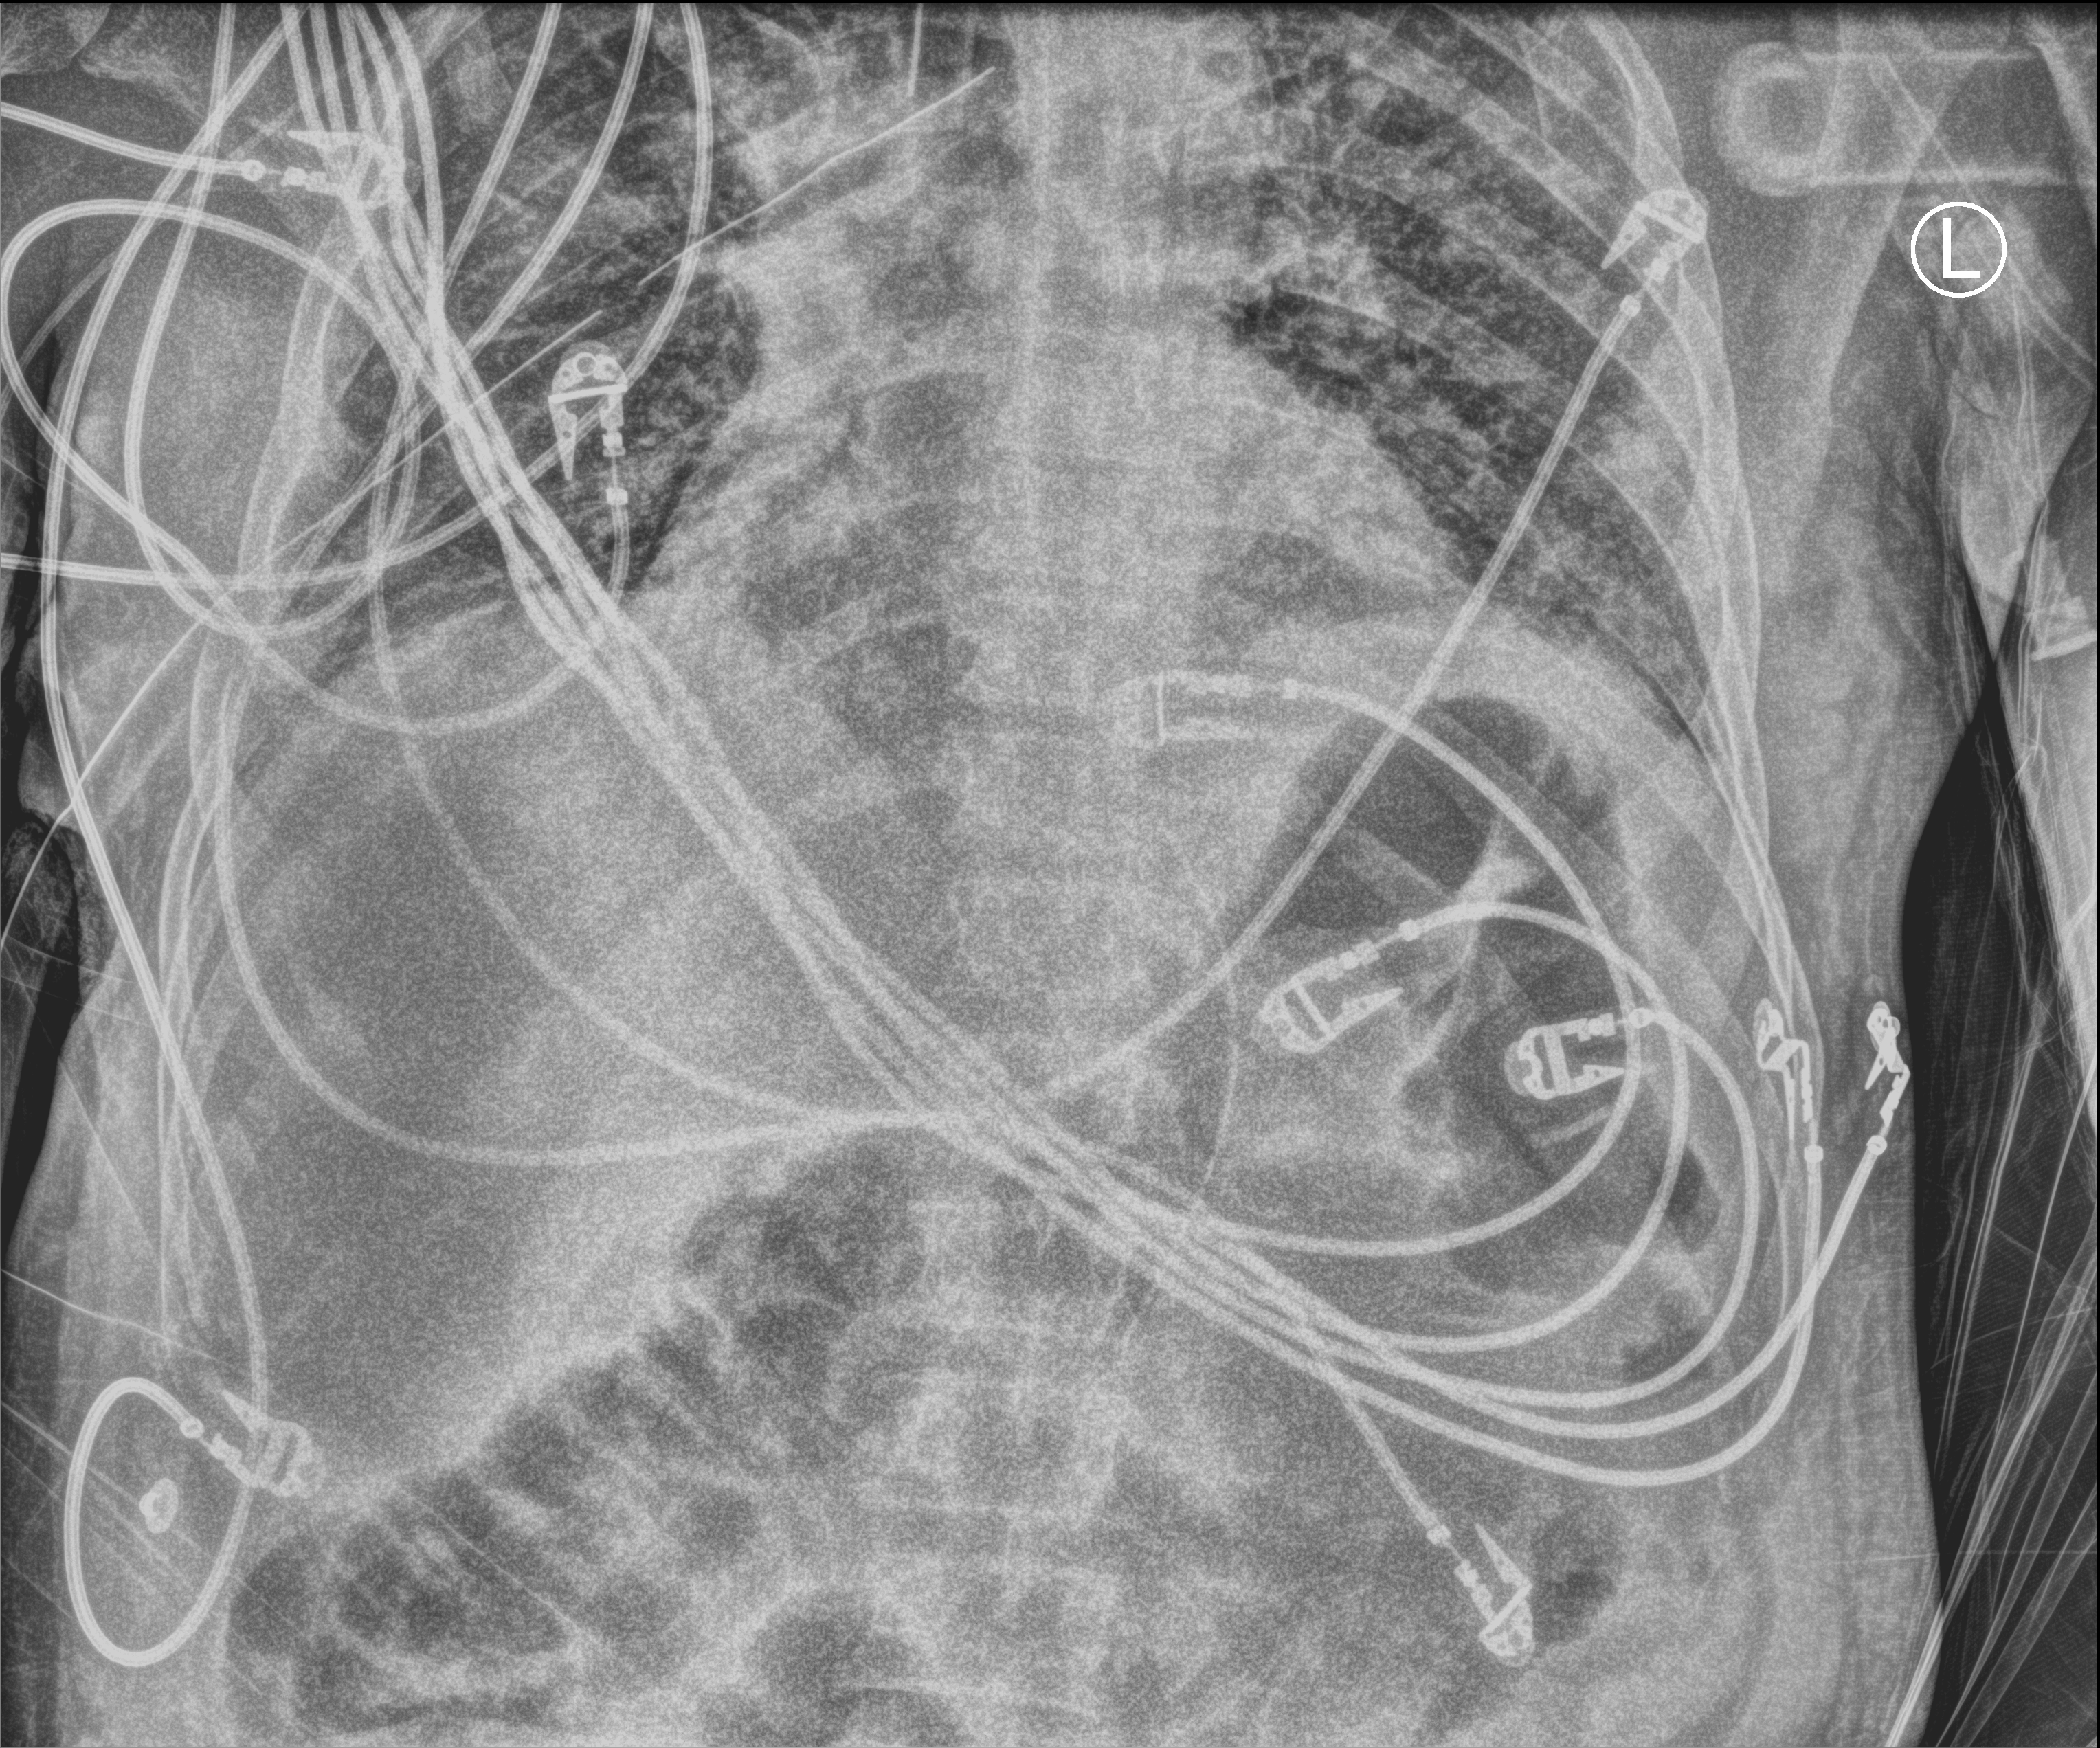
Chest X-ray (portable), anteroposterior (AP) projection. Male patient hospitalised with COVID-19, age 18–59 years.
Admission-level facts for this patient (not findings on this image; timing relative to this image not recorded): admitted to intensive care during this hospital stay: yes; other chronic lung disease (admission record): no.